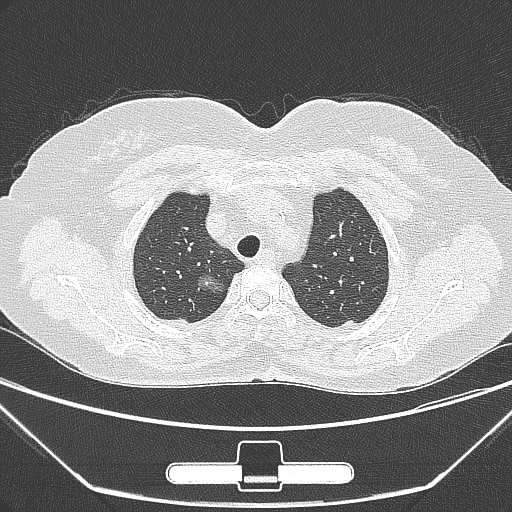
Chest CT, one axial slice; position 230 of 275 along the scan axis; lung window (W 1500 / L -600 HU); 1 mm slice thickness; 512 × 512 image matrix, field of view 356 × 356 mm. Female patient, age 63 years. From the clinical record (not read from this slice): clinical TNM (as recorded): T1a N0 M0; histopathological grade: G1.
Structures marked on this image (bounding box drawn by a radiologist):
- lung tumour (recorded histology: adenocarcinoma): box from (x=187, y=265) to (x=230, y=303) px